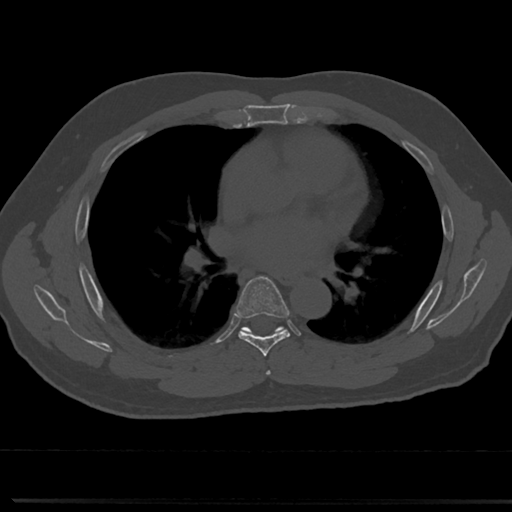
CT including the spine, one axial slice; position 444 of 817 along the scan axis; reconstruction kernel Br40s/3; 120 kVp; bone window (W 1800 / L 400 HU); 512 × 512 image matrix, field of view 355 × 355 mm. Patient: male, 61 years. From the clinical record (not read from this slice): primary cancer: prostate.
Outlined on this slice (semi-automatically segmented with operator editing):
- T5 vertebra: bounding box [x1, y1, x2, y2] px = [265, 354, 273, 377]
- T6 vertebra: [219, 277, 310, 353]